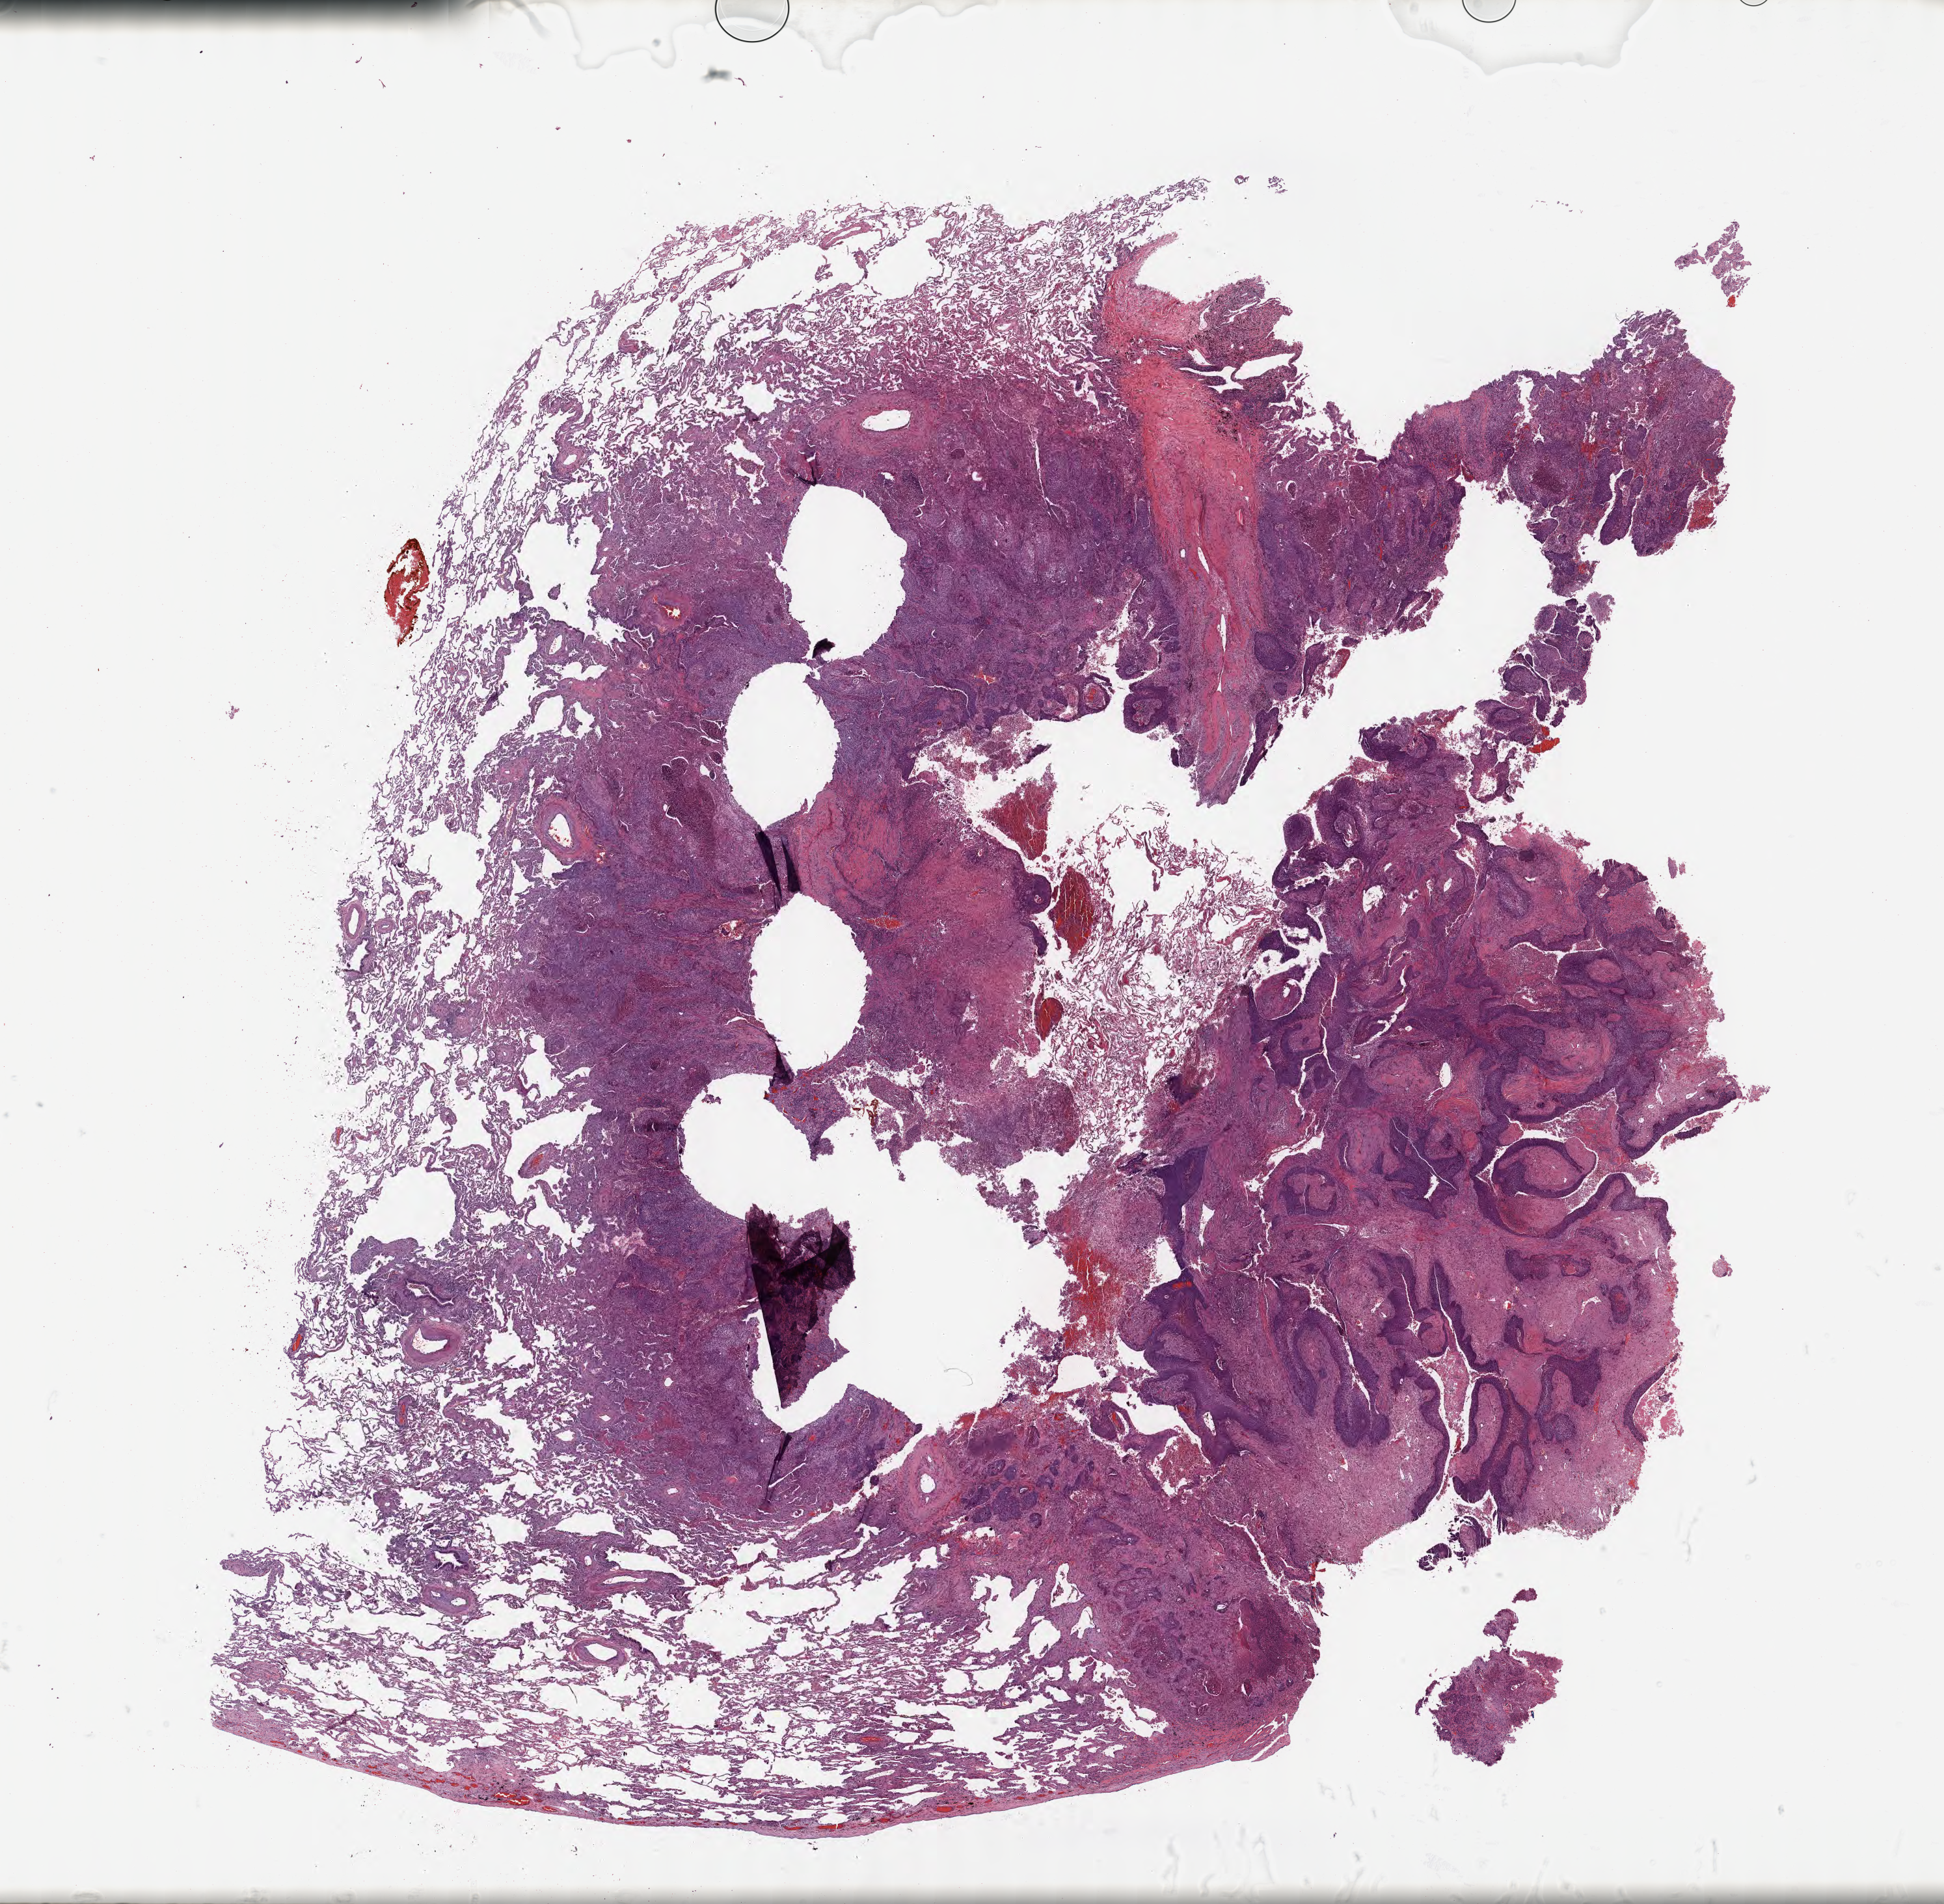
Haematoxylin and eosin whole-slide image, a low-resolution overview of the entire scanned area, about 24.1 x 23.7 mm. Specimen: tumor tissue. Site: lung. Patient sex: male.
Histologic diagnosis: Squamous cell carcinoma, NOS.